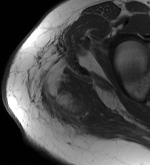
MRI of an extremity soft-tissue mass, one axial slice; slice 43 of 56 in the series (ordered by position); MR volume resampled by the dataset authors to the PET/CT grid (not the native acquisition matrix); 150 × 165 image matrix, field of view 146 × 161 mm. Female patient. From the clinical record (not read from this slice): histological type: epithelioid sarcoma with vascular differentiation; site of the primary tumour: right buttock.
Outlined on this slice (expert contour drawn on MRI and transferred to this co-registered scan by the dataset authors):
- gross tumour volume (mass): bounding box <43,79,90,109> (left, top, right, bottom; pixels)